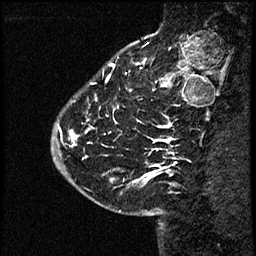
Breast MRI (dynamic contrast-enhanced), one sagittal slice. Position 15 of 60 along the scan axis. Dynamic contrast-enhanced study with each time point stored as its own series, time point 2 of 4 at this slice position (early post-contrast, ordered by acquisition time). 1.5 T. TE 4.2 ms, TR 17.6 ms. 2 mm slice thickness. 256 × 256 image matrix, field of view 200 × 200 mm. Female patient, age 43 years. From the clinical record (not read from this slice): setting: breast cancer imaged before/during neoadjuvant chemotherapy.
Annotated regions visible in this slice (semi-automatically segmented with operator editing):
- analysis volume of interest (the breast-tissue region the enhancement analysis was run in; not a lesion): box from (x=57, y=56) to (x=169, y=191) px
- tumour enhancement mask (voxels above the 100 % enhancement threshold inside the analysis volume of interest): (x=63, y=124)–(x=169, y=181)